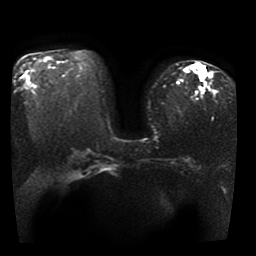
Breast MRI, one axial slice. Position 23 of 41 along the scan axis. Diffusion-weighted series; image 2 of 4 stored at this slice position (different b-values; order by instance number). 1.5 T. 5 mm slice thickness. 256 × 256 image matrix, field of view 330 × 330 mm. Female patient.
Annotated regions visible in this slice (outlined manually by an expert reader):
- tumour on diffusion-weighted imaging: bounding box (x1, y1, x2, y2) in pixels: (190, 67, 204, 78)